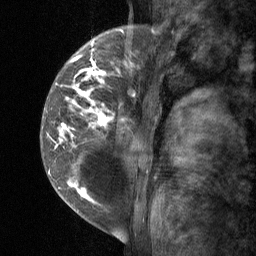
Breast MRI (dynamic contrast-enhanced), one sagittal slice. Slice 16 of 64 in the series (ordered by position). Dynamic contrast-enhanced study with each time point stored as its own series, time point 2 of 3 at this slice position (early post-contrast, ordered by acquisition time). 1.5 T. TE 4.8 ms, TR 27 ms. 2 mm slice thickness. 256 × 256 image matrix. Female patient, age 34 years. From the clinical record (not read from this slice): setting: breast cancer imaged before/during neoadjuvant chemotherapy; receptor status: HR-positive, HER2-negative.
Annotated regions visible in this slice (semi-automatically segmented with operator editing):
- analysis volume of interest (the breast-tissue region the enhancement analysis was run in; not a lesion): bounding box [x1, y1, x2, y2] px = [41, 23, 157, 197]
- tumour enhancement mask (voxels above the 90 % enhancement threshold inside the analysis volume of interest): [47, 30, 156, 197]